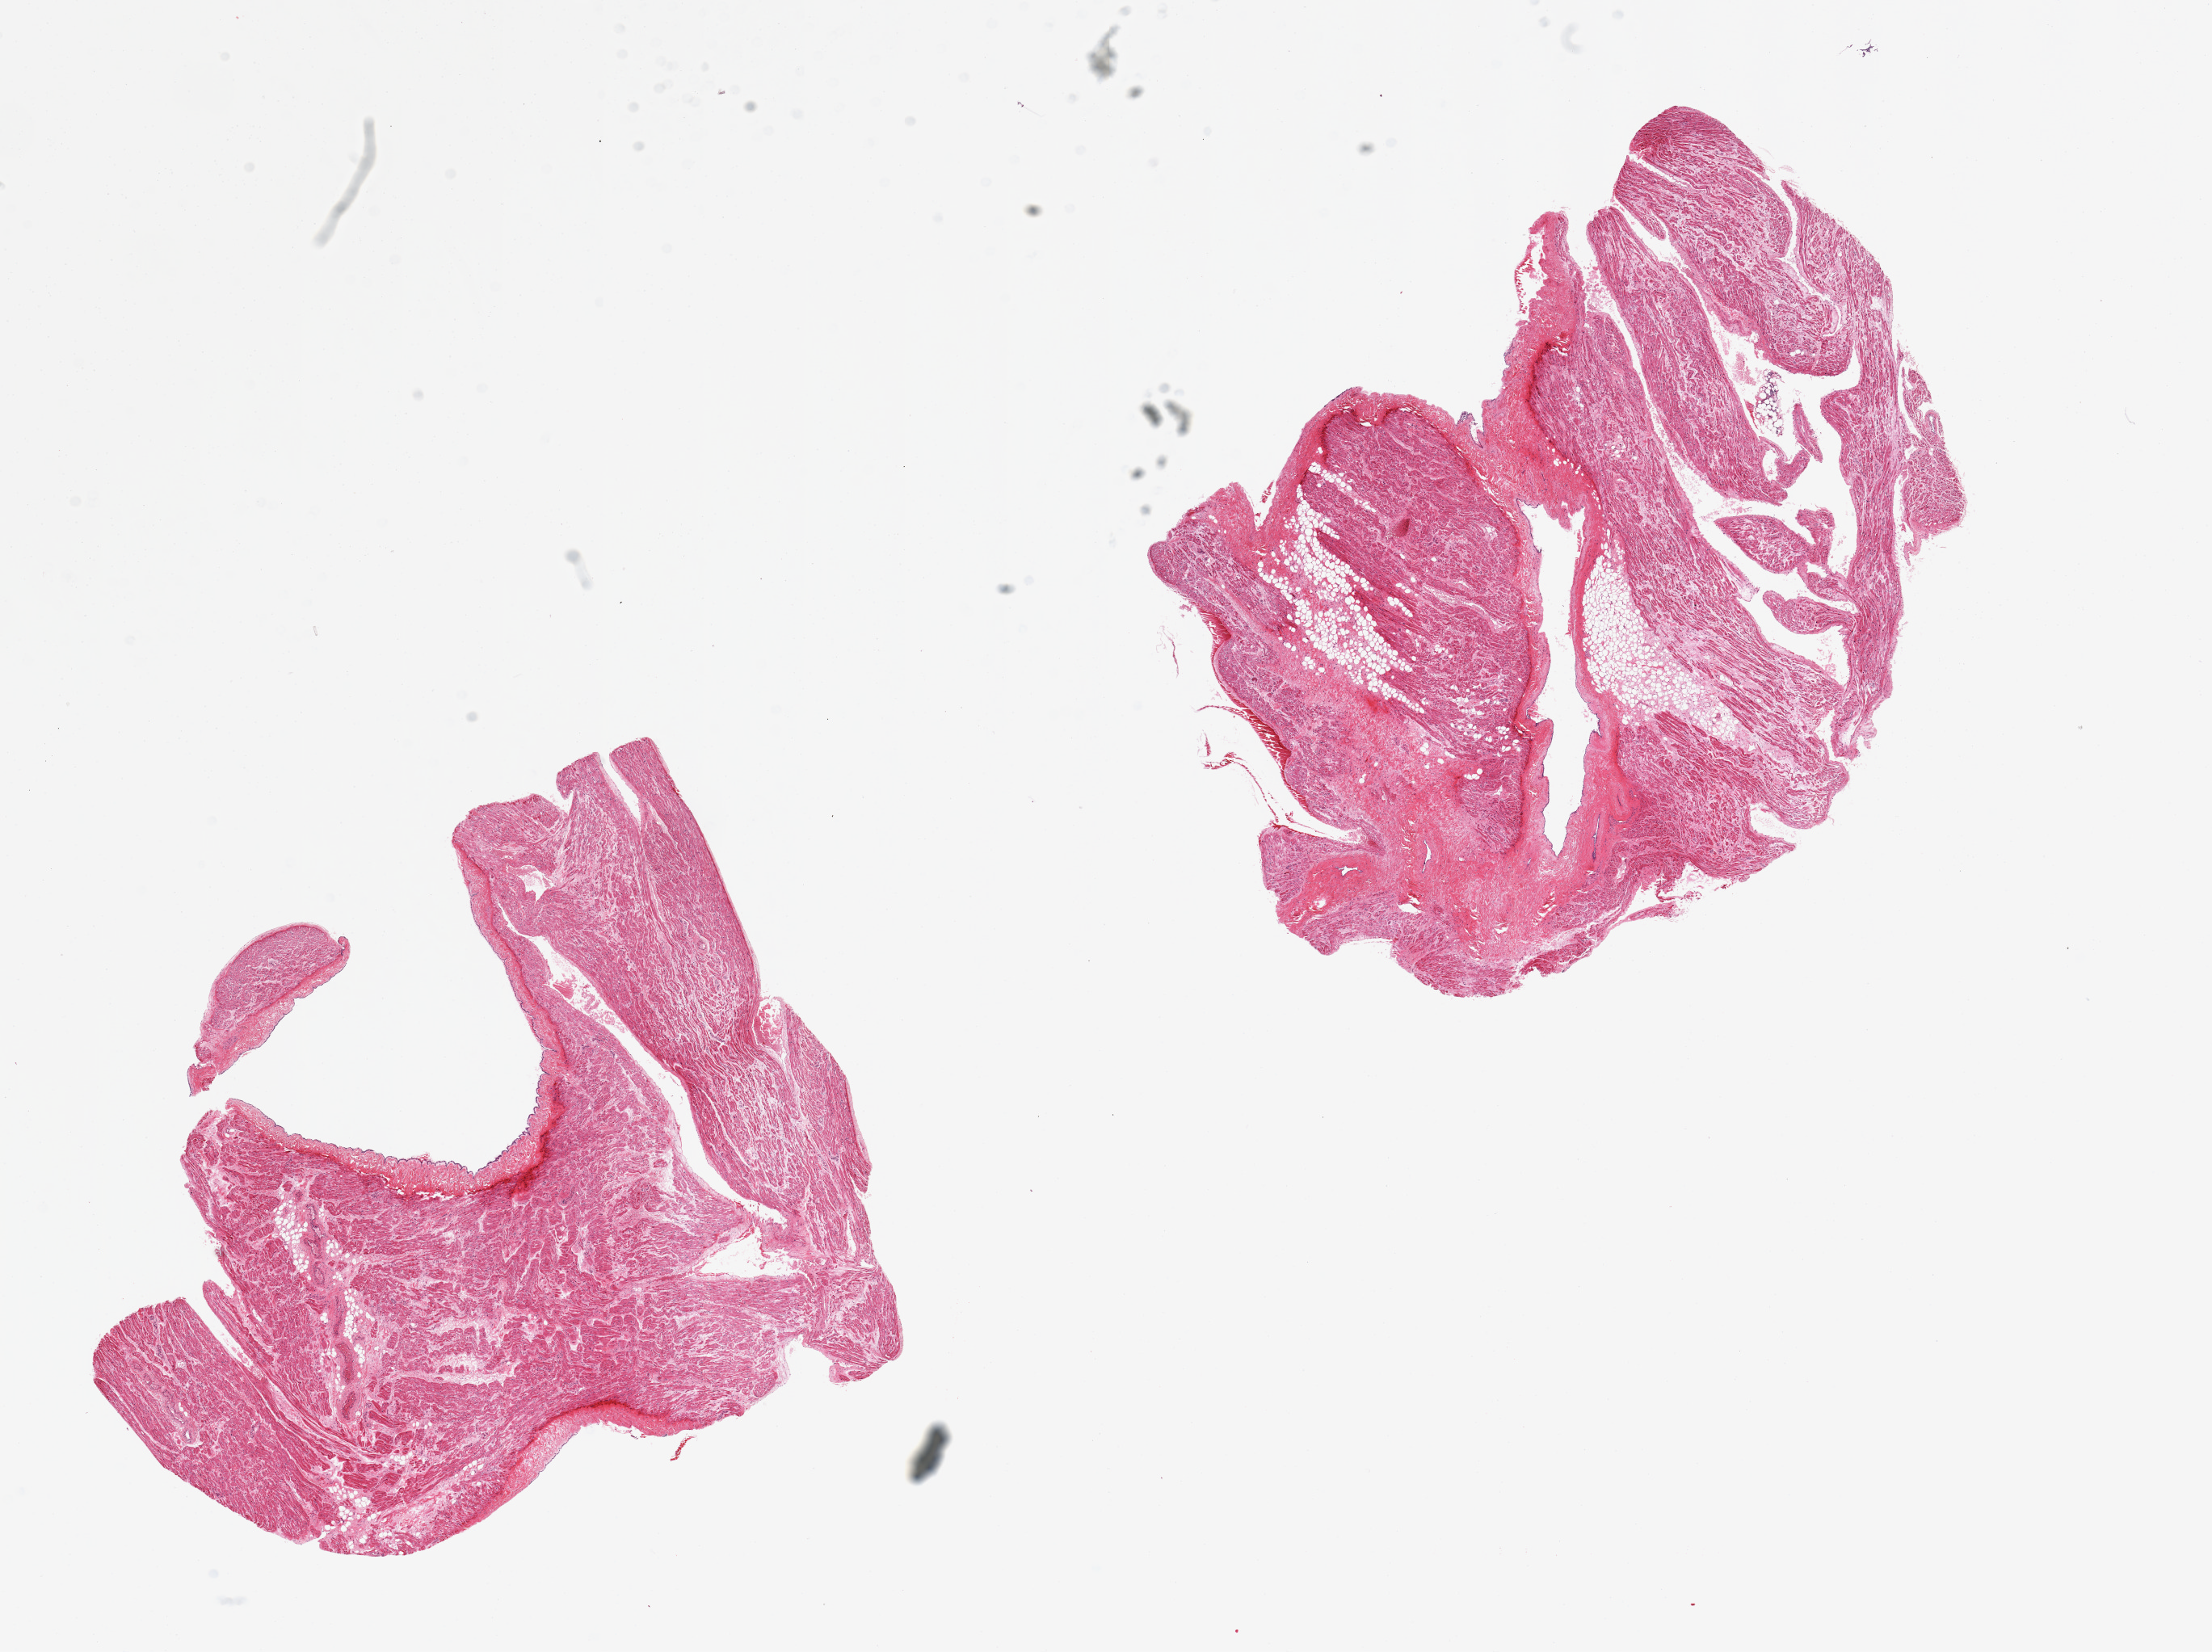
Whole-slide image, haematoxylin and eosin stain, brightfield, low-resolution overview of the scanned area, about 21.7 x 16.2 mm (from a 20x scan), PAXgene-fixed, paraffin-embedded tissue, section of auricular appendage (target tissue), donor tissue sample. Donor sex: male.
- review note (as recorded): 2 pieces; one with 30% fat and fibrous tissue